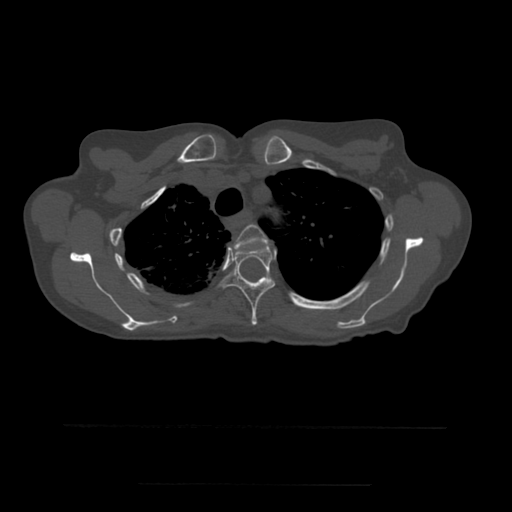
CT including the spine, one axial slice. Position 409 of 544 along the scan axis. Bone window (W 1800 / L 400 HU). 1.25 mm slice thickness. 512 × 512 image matrix. Patient age 58 years. From the clinical record (not read from this slice): primary cancer: lung.
Outlined on this slice (semi-automatic segmentation, software-assisted and operator-edited):
- T3 vertebra: bounding box (x1, y1, x2, y2) in pixels: (234, 225, 268, 251)
- T4 vertebra: (218, 244, 275, 326)